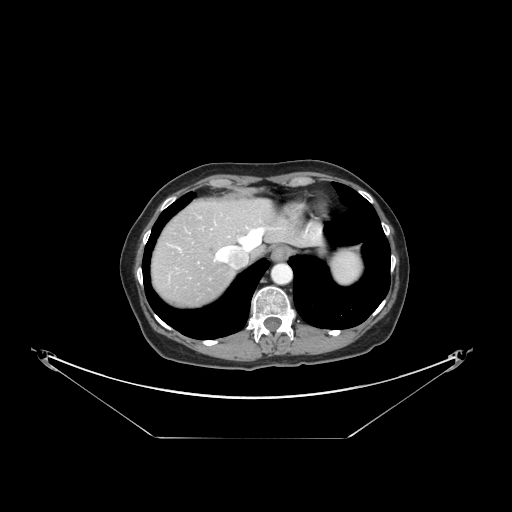
Contrast-enhanced abdominal CT, one axial slice; slice 127 of 148 in the series (ordered by position); reconstruction kernel STANDARD; intravenous contrast given; soft-tissue window (W 400 / L 40 HU); 2.5 mm slice thickness; 512 × 512 image matrix, field of view 500 × 500 mm. Female patient, age 73 years. From the clinical record (not read from this slice): diagnosis: colorectal cancer liver metastases, imaged before liver resection; multiple liver metastases: no; largest metastasis: 1 cm; disease in both lobes: no.
Structures marked on this image (outlined manually by an expert reader):
- hepatic veins: bounding box [x1, y1, x2, y2] px = [216, 227, 283, 262]
- liver: [152, 199, 296, 307]
- planned liver remnant (the part of the liver to remain after resection): [180, 199, 296, 249]
- liver metastasis: [208, 245, 216, 254]